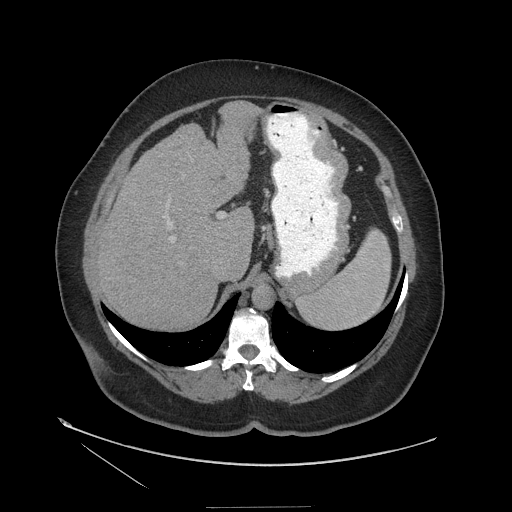
Contrast-enhanced abdominal CT (liver protocol), one axial slice. Slice 83 of 127 in the series (ordered by position). Reconstruction kernel STANDARD. Soft-tissue window (W 400 / L 40 HU). 512 × 512 image matrix, field of view 480 × 480 mm. Case-level facts recorded for this patient, not image findings: diagnosis: hepatocellular carcinoma (patient treated with transarterial chemoembolisation; whether this scan precedes or follows treatment is not stated here); TNM stage (as recorded): Stage-II; Child-Pugh class: A; tumour differentiation: well differentiated; tumour nodularity: multinodular.
Annotated regions visible in this slice (semi-automatic segmentation, software-assisted and operator-edited):
- liver parenchyma outside the tumour (the mass and vessels are separate outlines, so this box may not span the whole liver): bounding box [x1, y1, x2, y2] px = [98, 103, 260, 328]
- liver vessels: [167, 214, 224, 241]